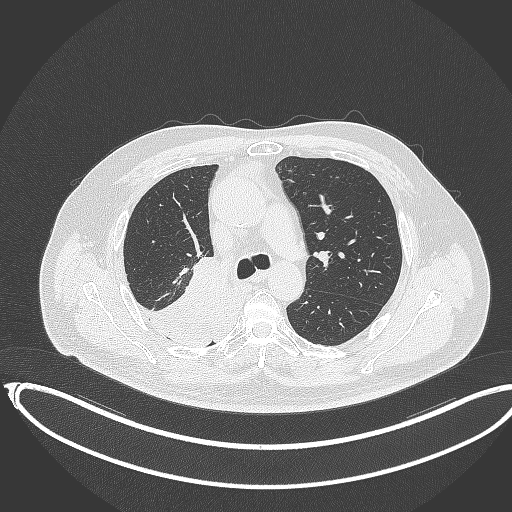
Chest CT, one axial slice. 120 kVp. Lung window (W 1500 / L -600 HU). 1 mm slice thickness. 512 × 512 image matrix, field of view 436 × 436 mm. Patient: male, 68 years. Case-level facts recorded for this patient, not image findings: clinical TNM (as recorded): T2a N0 M0.
Annotated regions visible in this slice (rectangle marked by the reading radiologist):
- lung tumour (recorded histology: adenocarcinoma): box from (x=127, y=256) to (x=230, y=347) px